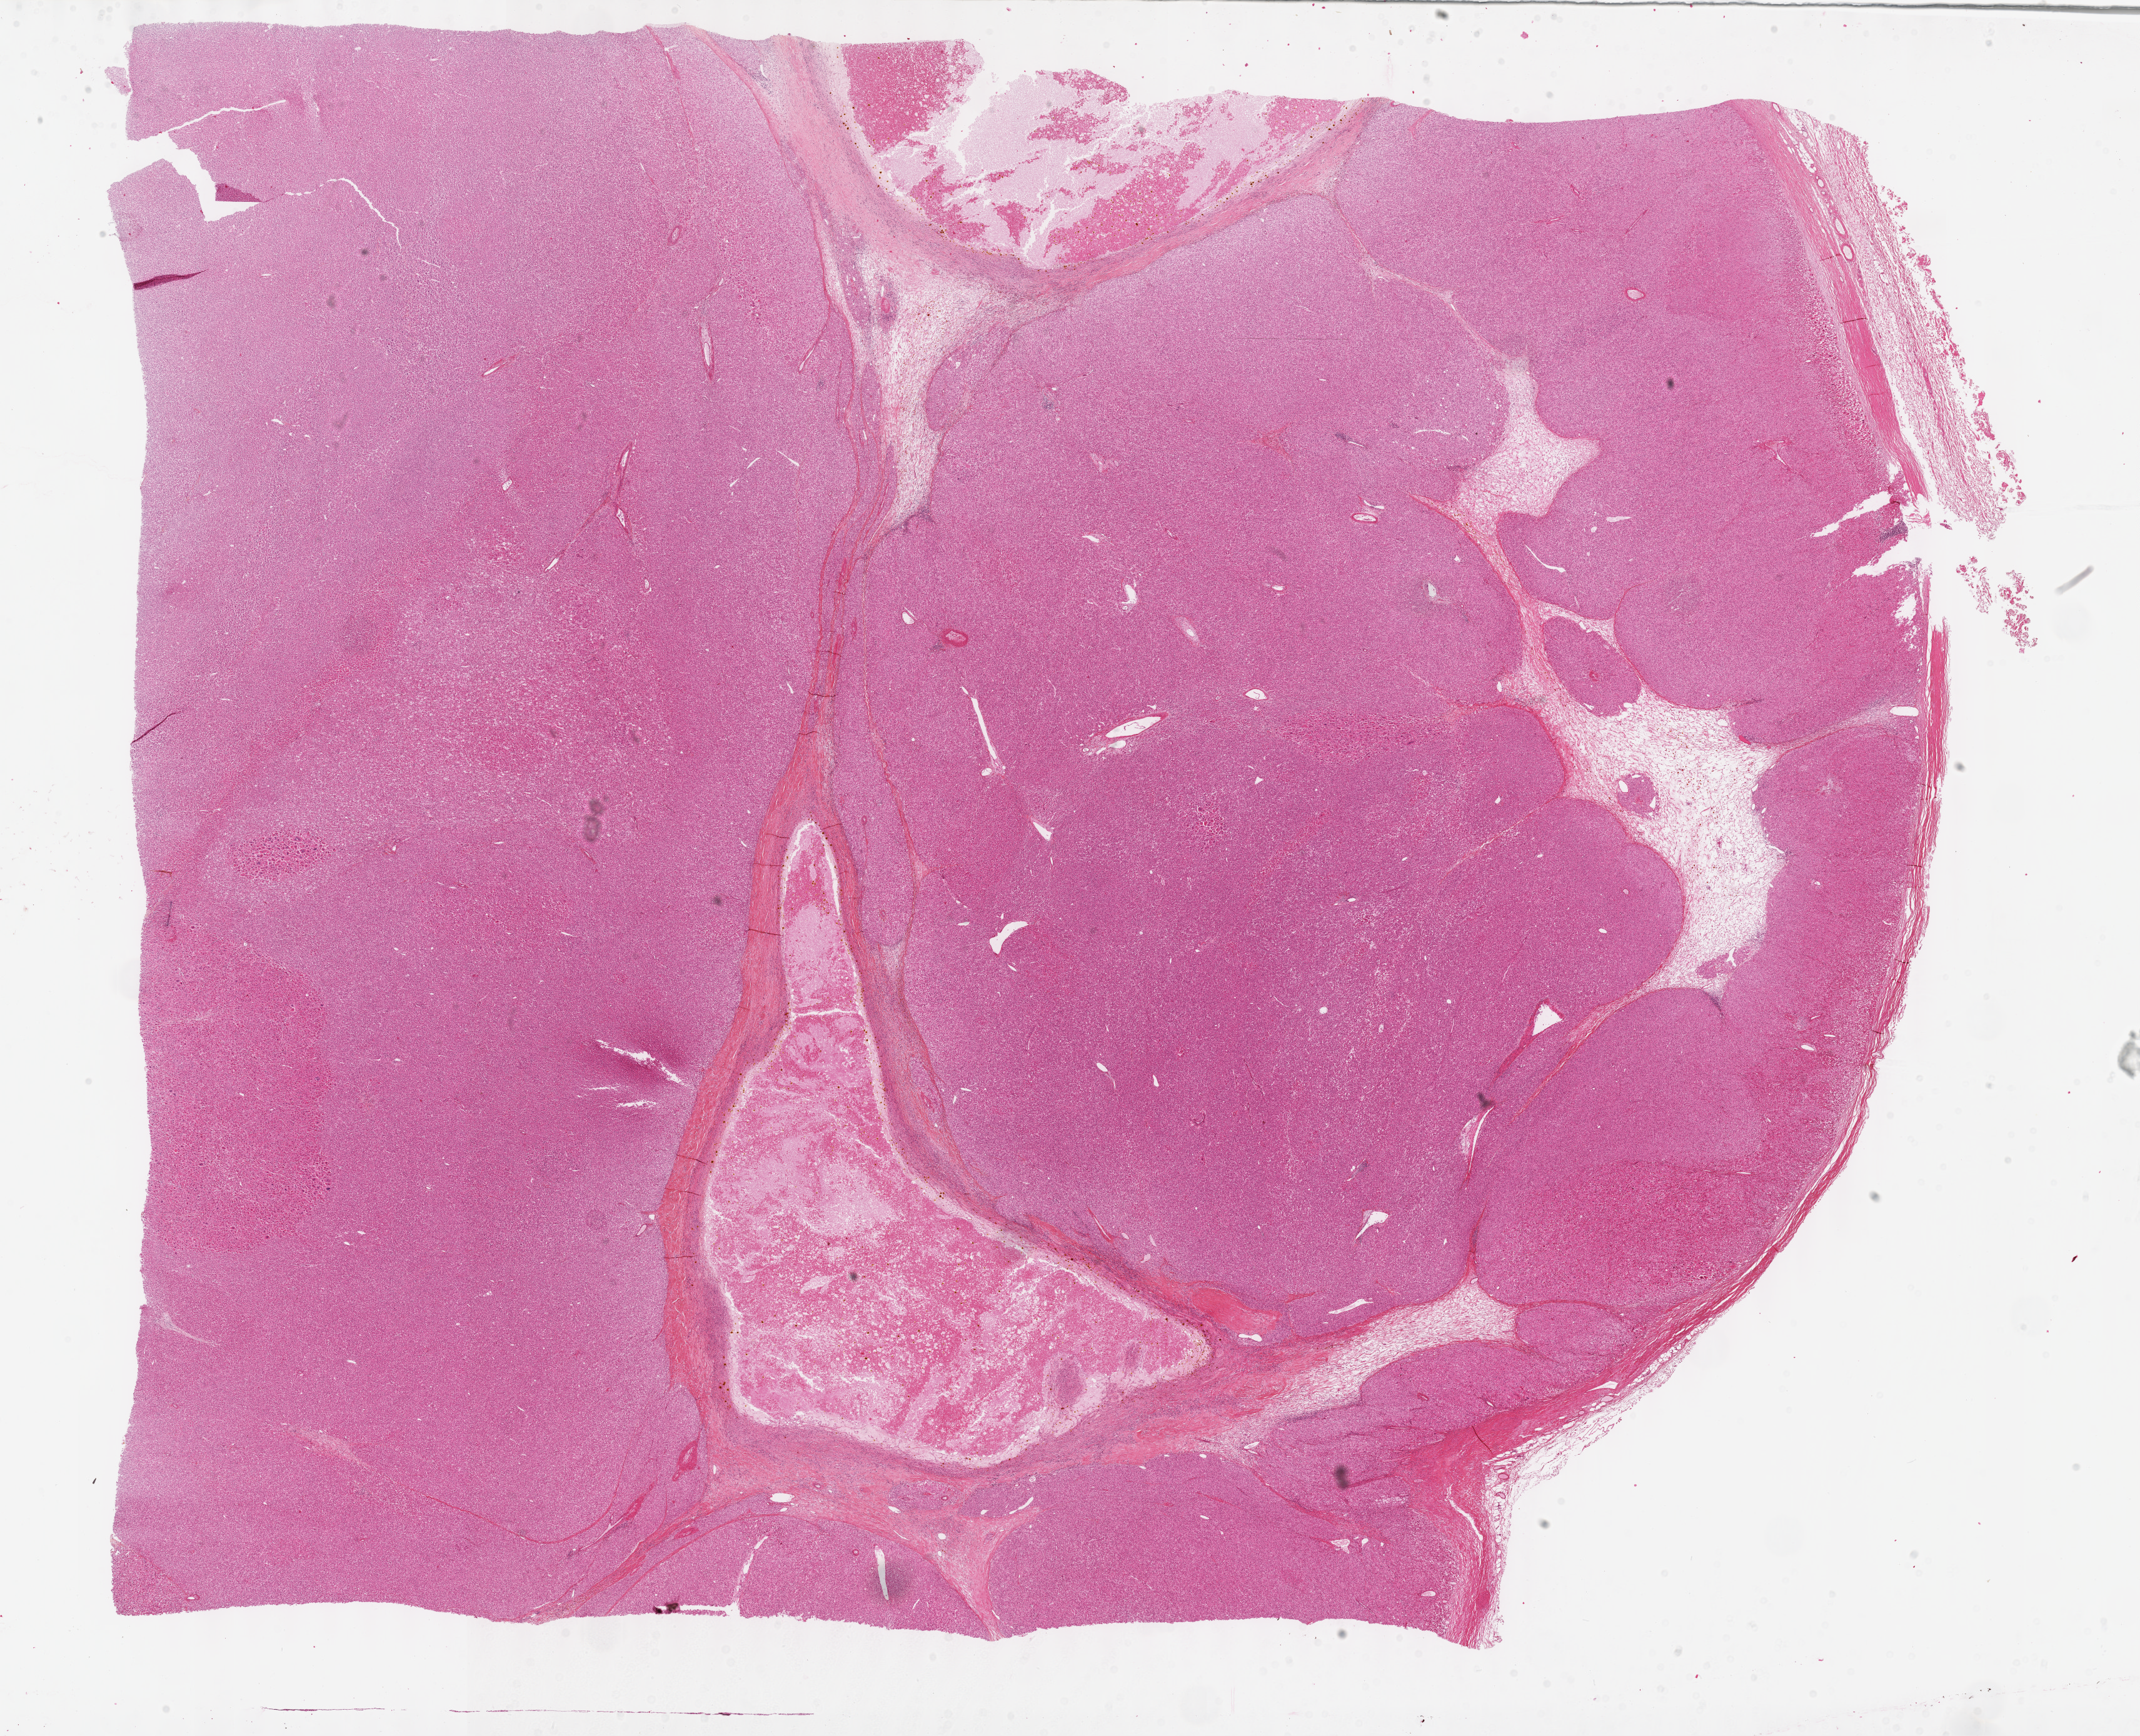
H&E-stained whole-slide image — whole scanned area (about 27.7 x 22.4 mm) shown as a low-resolution overview. Formalin-fixed paraffin-embedded (FFPE) diagnostic section. Sample: primary tumour, adrenal cortex. Patient: female, age at initial diagnosis 30 years.
Histologic diagnosis: Adrenal cortical carcinoma (cortex of adrenal gland).